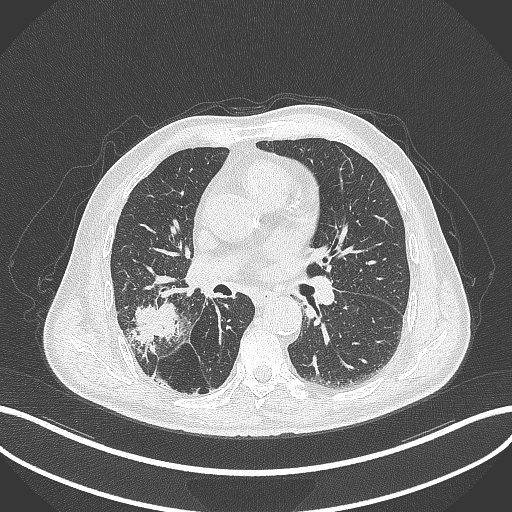
Chest CT, one axial slice; position 221 of 429 along the scan axis; lung window (W 1500 / L -600 HU); 512 × 512 image matrix, field of view 400 × 400 mm. Patient: male, 72 years. From the clinical record (not read from this slice): clinical TNM (as recorded): T3 N2 M0.
Annotated regions visible in this slice (rectangle marked by the reading radiologist):
- lung tumour (recorded histology: adenocarcinoma): box from (x=125, y=296) to (x=182, y=348) px